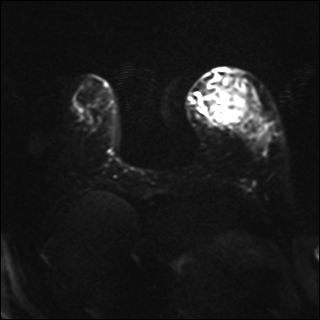
Breast MRI, one axial slice; slice 9 of 37 in the series (ordered by position); diffusion-weighted series; image 2 of 4 stored at this slice position (different b-values; order by instance number); 1.5 T; 4 mm slice thickness; 320 × 320 image matrix, field of view 320 × 320 mm. Female patient.
Outlined on this slice (manually delineated by an expert):
- tumour on diffusion-weighted imaging: bounding box [x1, y1, x2, y2] px = [218, 88, 251, 126]